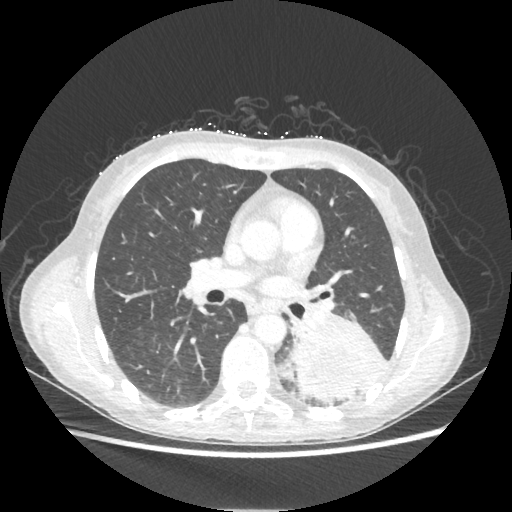
Chest CT, one axial slice. Position 121 of 221 along the scan axis. Reconstruction kernel STANDARD. Lung window (W 1500 / L -600 HU). 1.25 mm slice thickness. 512 × 512 image matrix. Patient: female, 53 years. From the clinical record (not read from this slice): clinical TNM (as recorded): T3 N0 M0.
Annotated regions visible in this slice (rectangle marked by the reading radiologist):
- lung tumour (recorded histology: adenocarcinoma): bounding box [x1, y1, x2, y2] px = [288, 310, 387, 403]